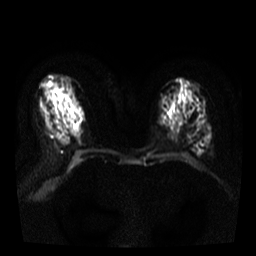
Breast MRI, one axial slice; slice 17 of 38 in the series (ordered by position); diffusion-weighted series; image 2 of 4 stored at this slice position (different b-values; order by instance number); 3 T; 256 × 256 image matrix, field of view 320 × 320 mm. Female patient.
Outlined on this slice (outlined manually by an expert reader):
- tumour on diffusion-weighted imaging: bounding box [x1, y1, x2, y2] px = [197, 150, 203, 156]